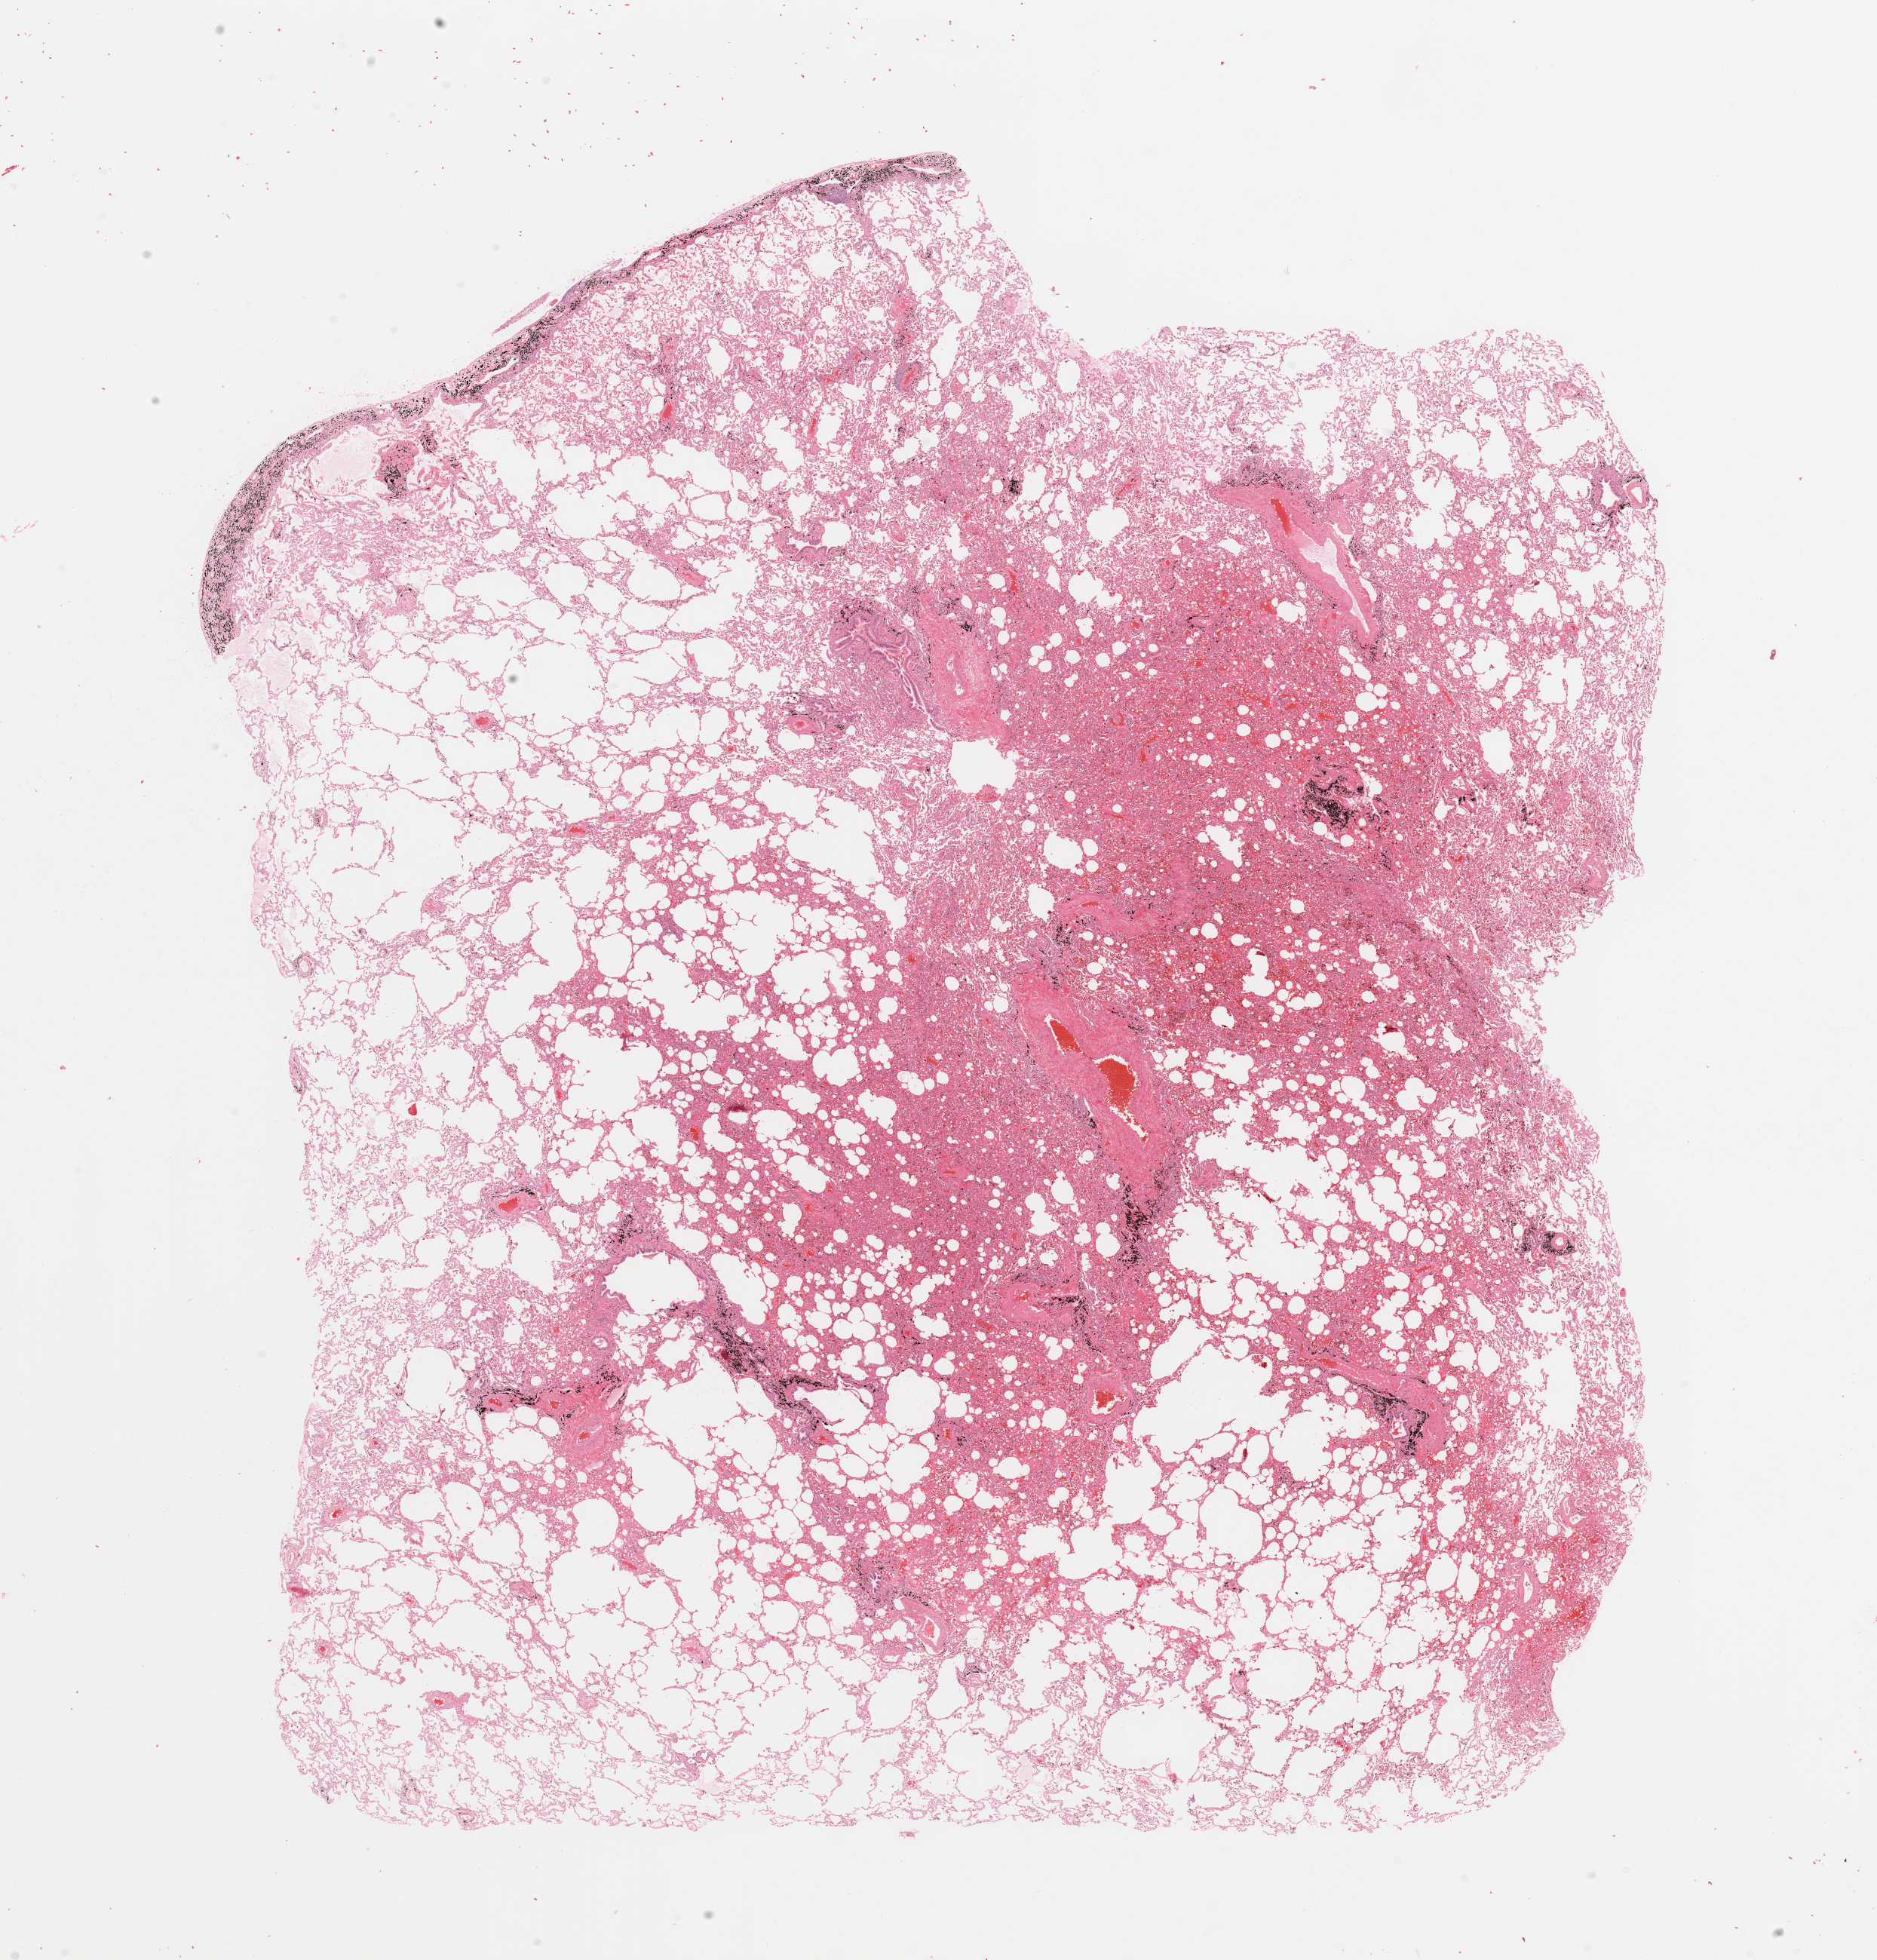
Whole-slide histology image, Hematoxylin and eosin (H&E) stained, shown as a low-resolution overview of the whole scanned area (about 19.7 x 20.6 mm). Lung, normal (non-tumour) tissue. 60-year-old male patient.
This section: normal (non-tumour) tissue from the same patient. Patient diagnosis: Adenocarcinoma, NOS.